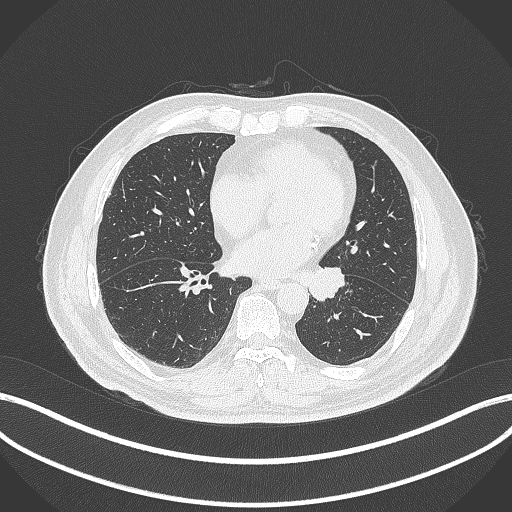
Chest CT, one axial slice. Position 117 of 312 along the scan axis. Reconstruction kernel B70f. 120 kVp. Lung window (W 1500 / L -600 HU). 1 mm slice thickness. 512 × 512 image matrix. Patient: male, 71 years. Case-level facts recorded for this patient, not image findings: clinical TNM (as recorded): T1b N0 M0.
Structures marked on this image (bounding box drawn by a radiologist):
- lung tumour (recorded histology: squamous cell carcinoma): bounding box (x1, y1, x2, y2) in pixels: (307, 265, 348, 304)